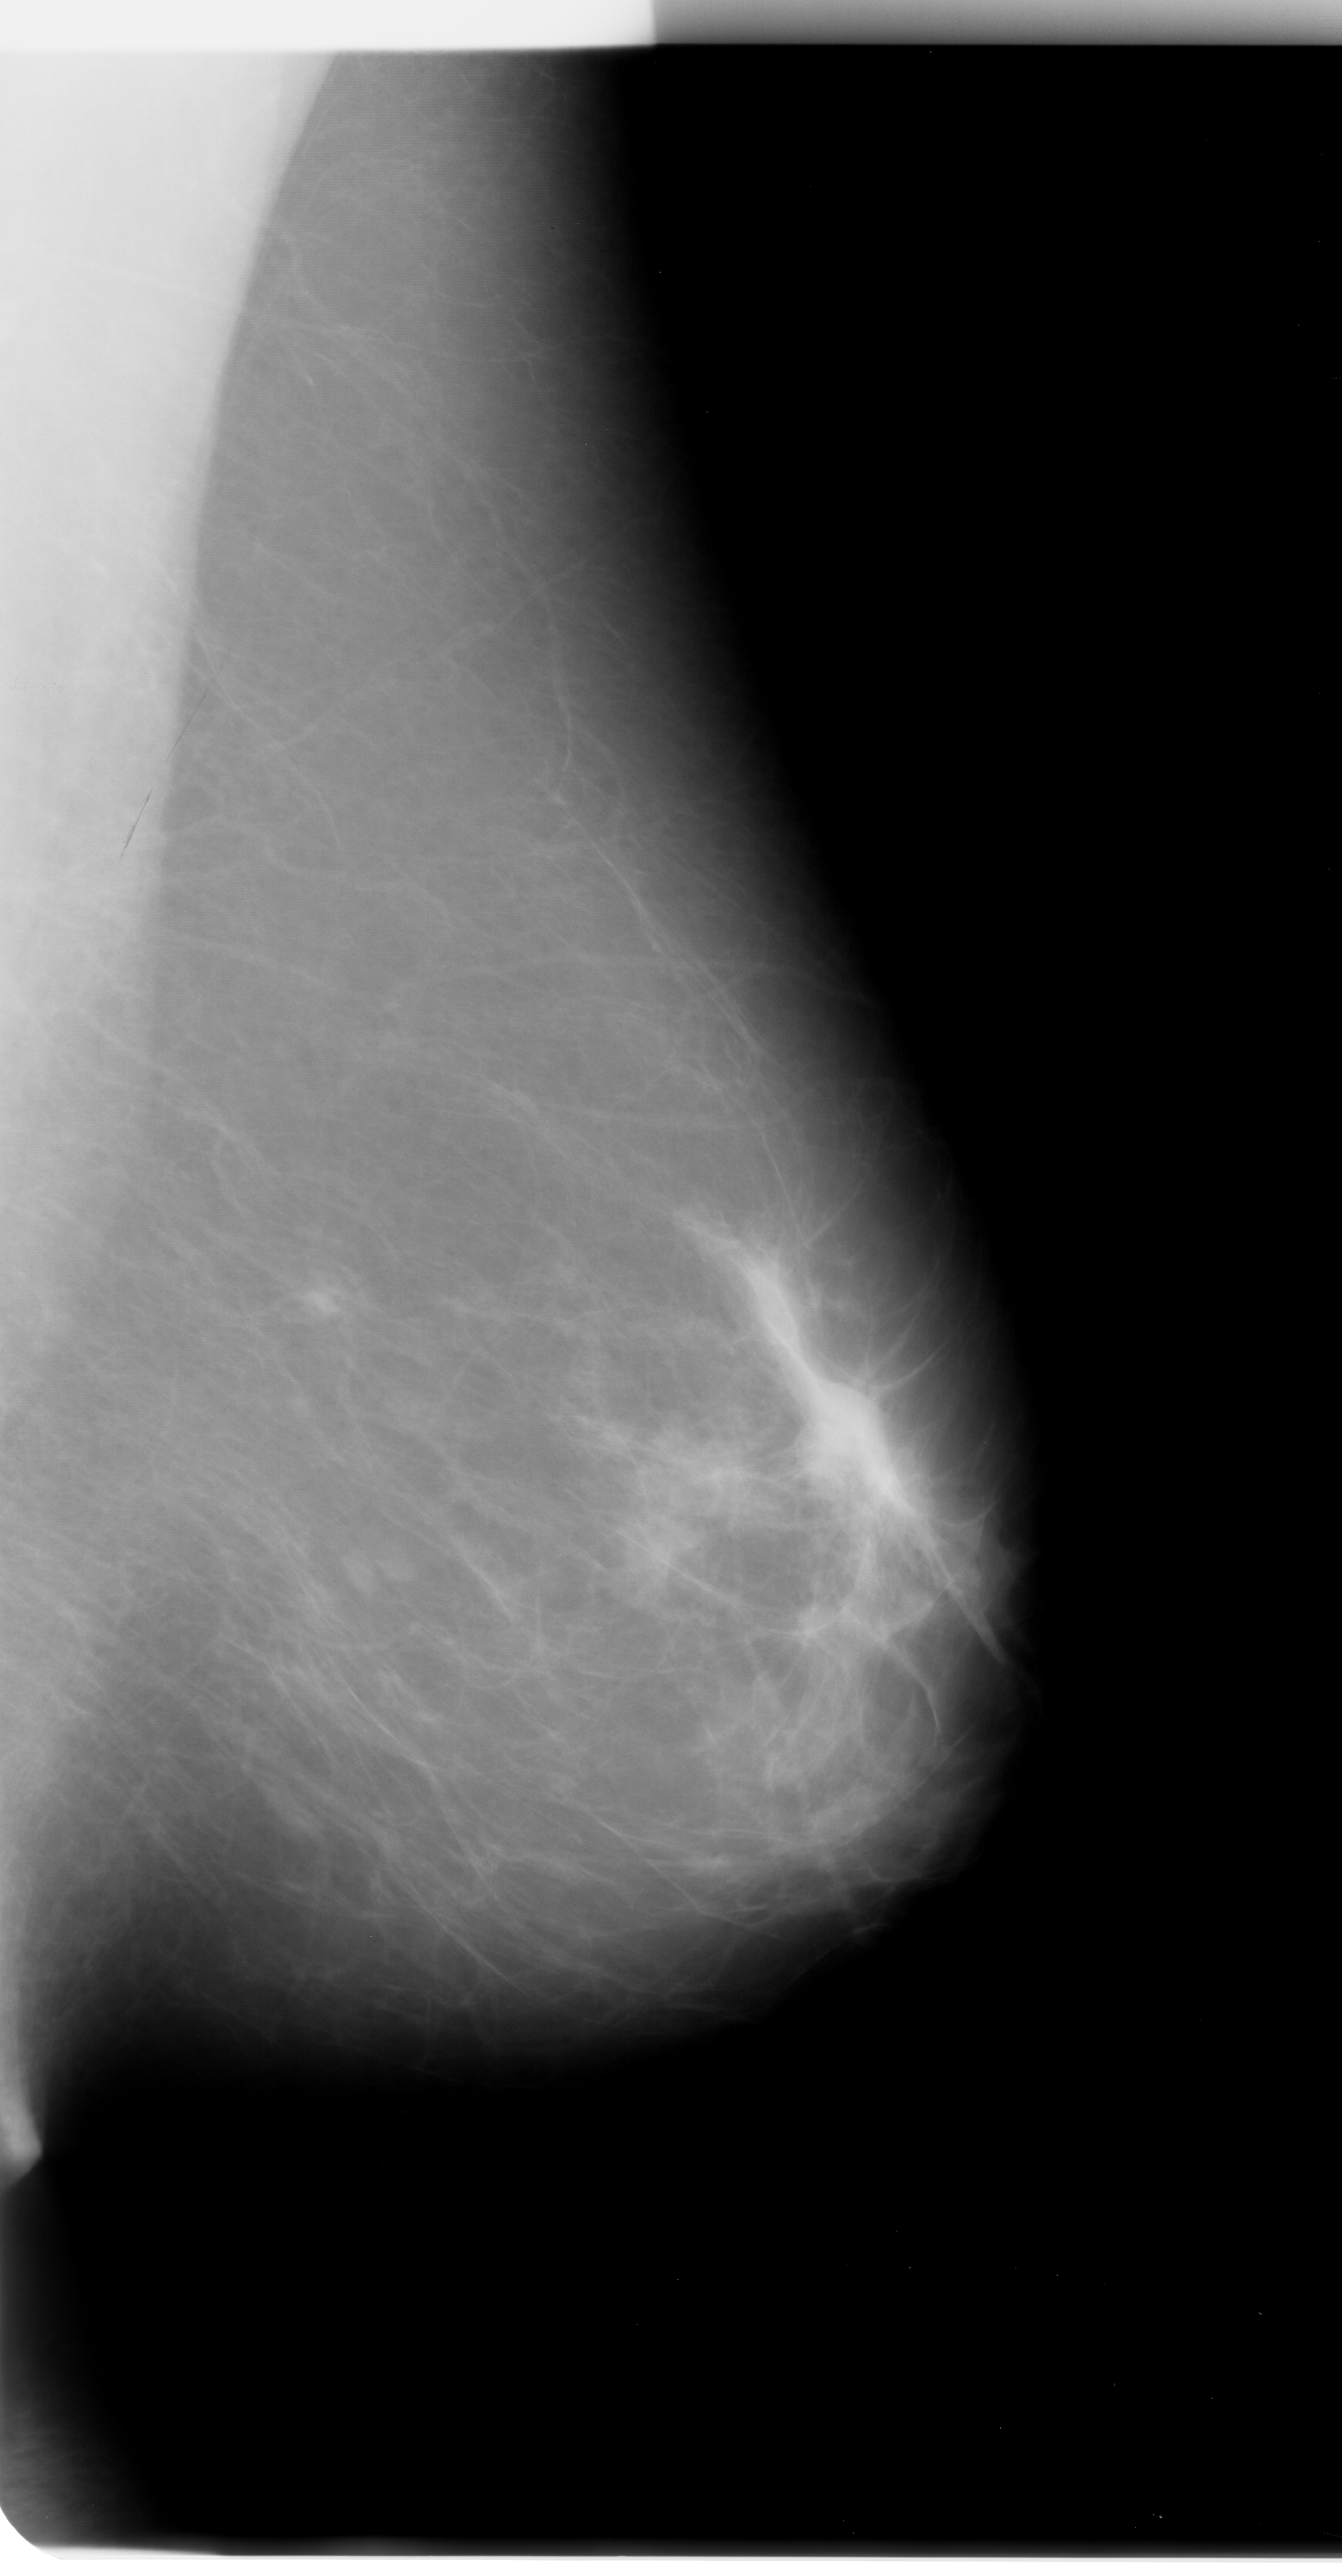
Scanned film-screen mammogram, left breast, mediolateral oblique (MLO) view, breast composition: almost entirely fatty (BI-RADS density category 1 of 4).
Mass, shape lobulated, margins obscured; BI-RADS assessment category 3; pathology result (as recorded, not read from the image): malignant.